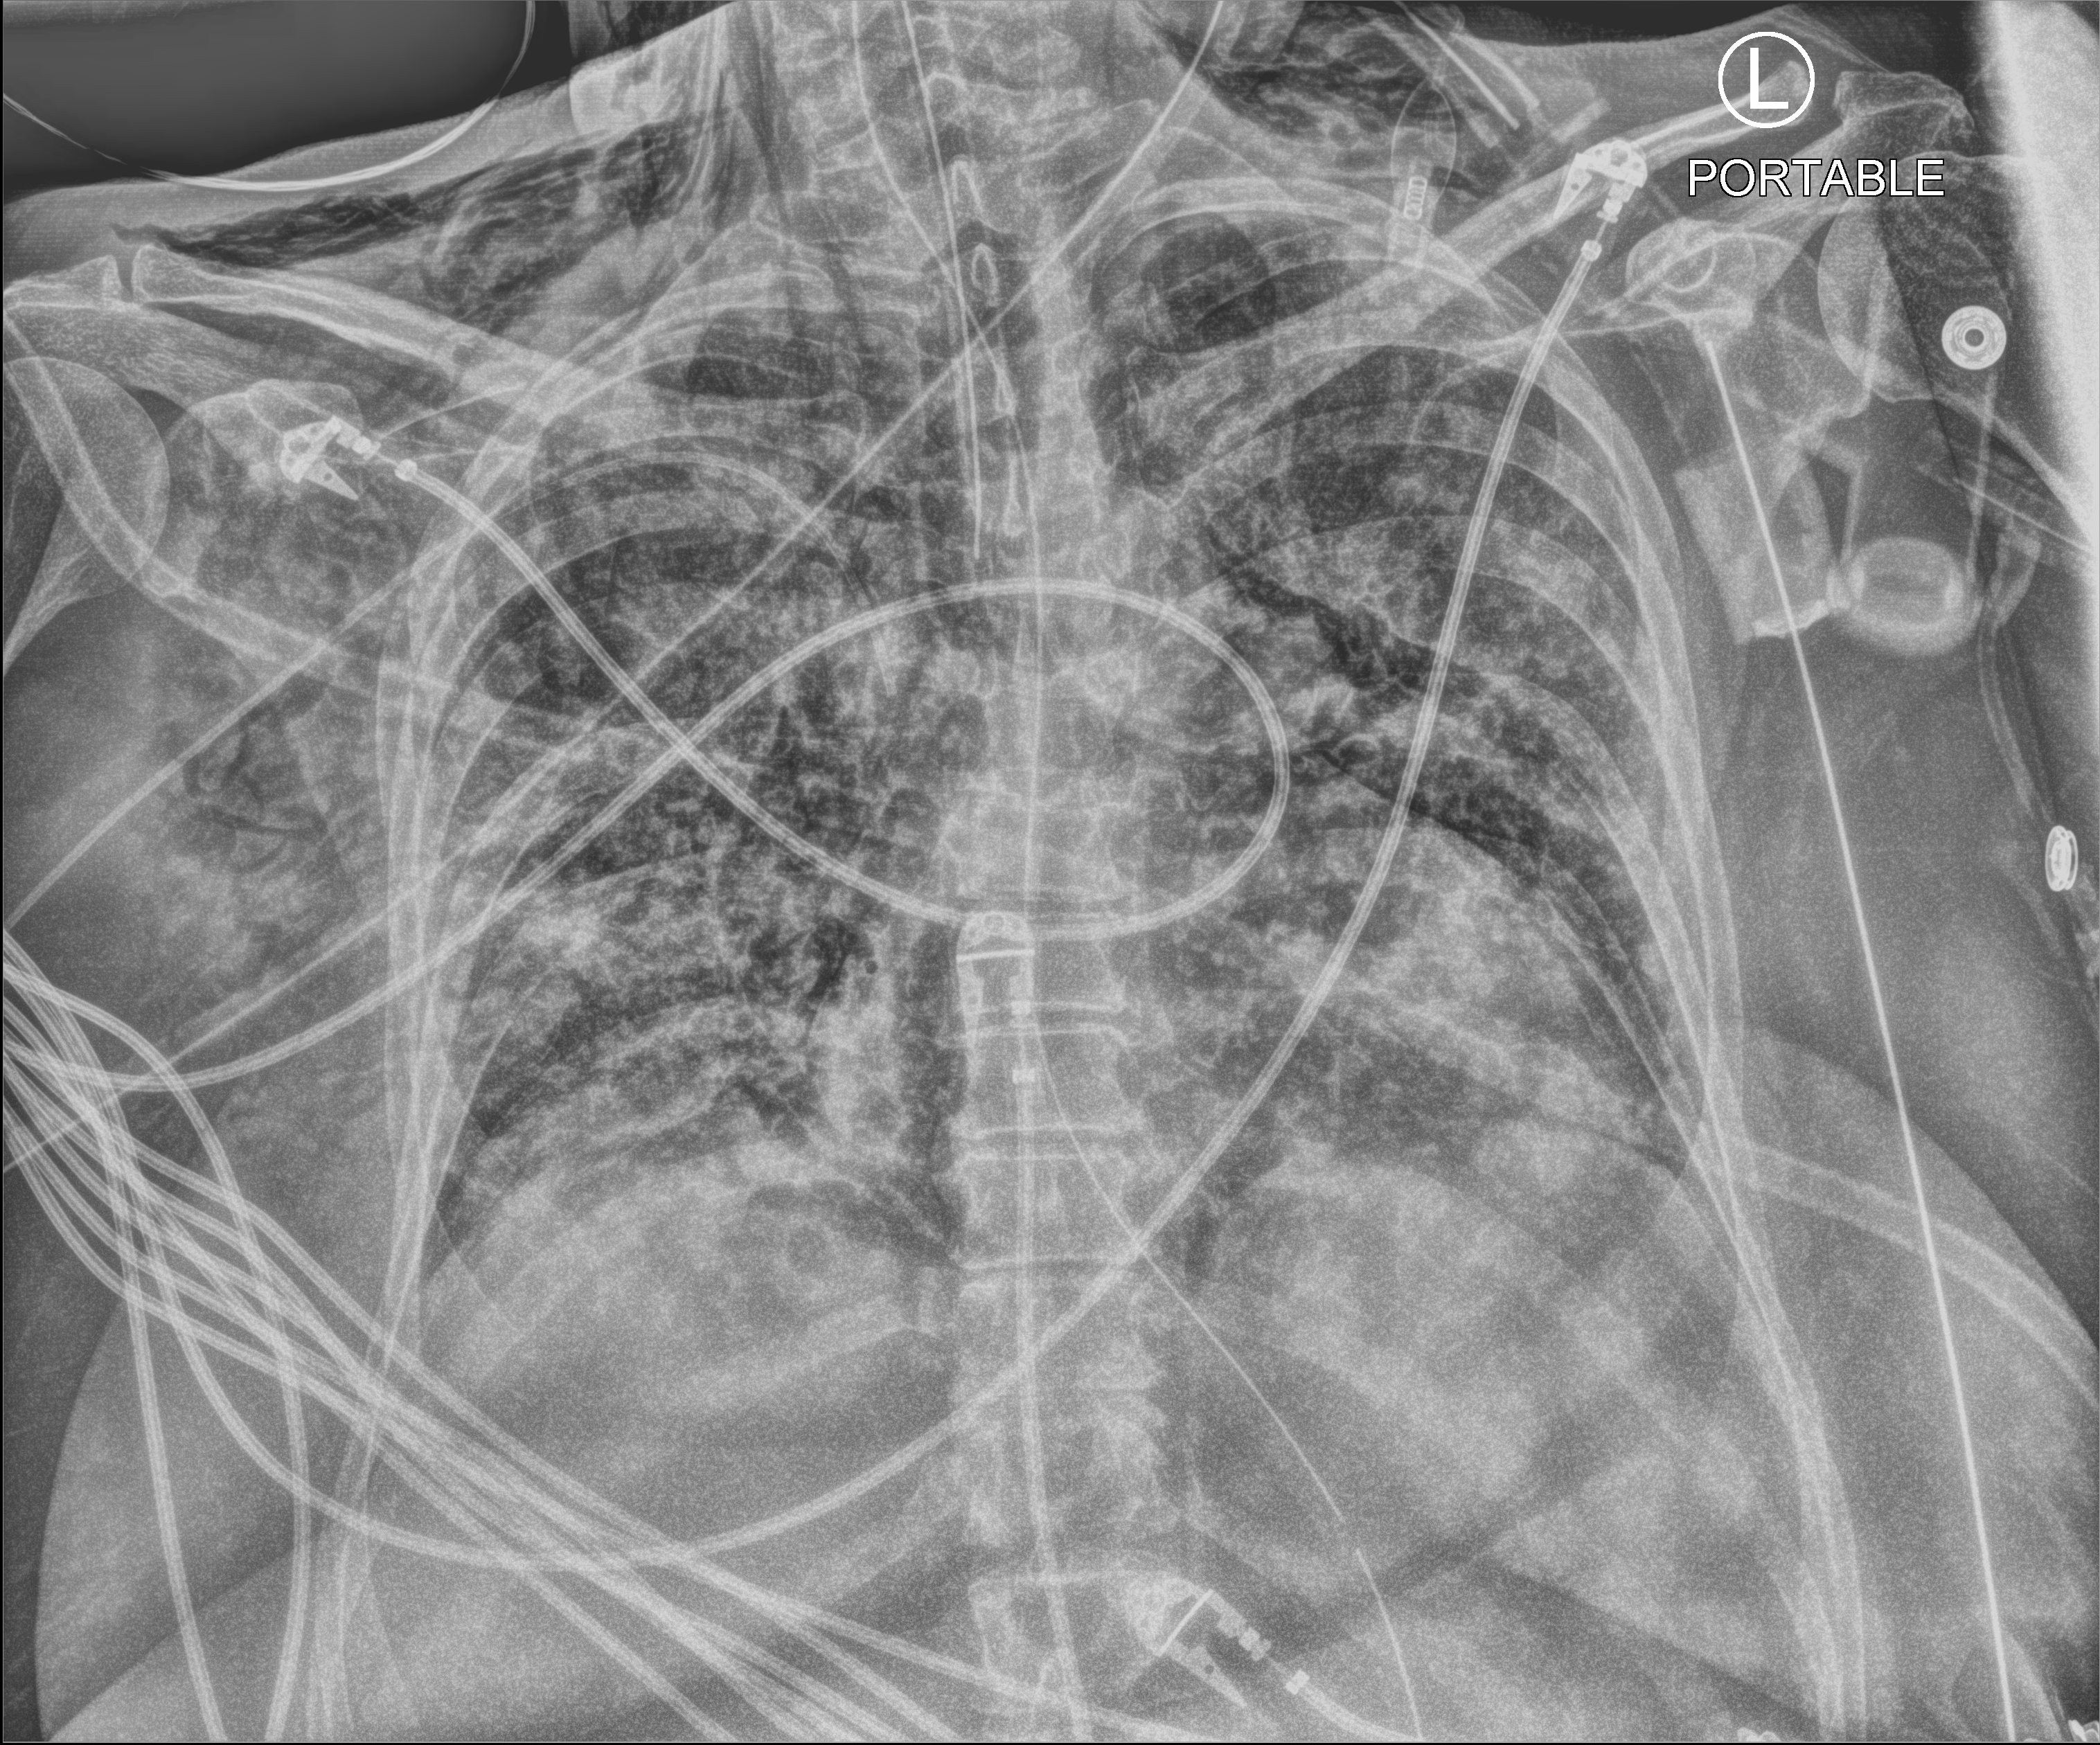
Chest X-ray (portable), anteroposterior (AP) projection. Female patient hospitalised with COVID-19, age 60–74 years.
Hospital-stay facts (about this admission, not read from this image; timing relative to this image not recorded): mechanically ventilated during this hospital stay: yes; admitted to intensive care during this hospital stay: yes; other chronic lung disease (admission record): yes.